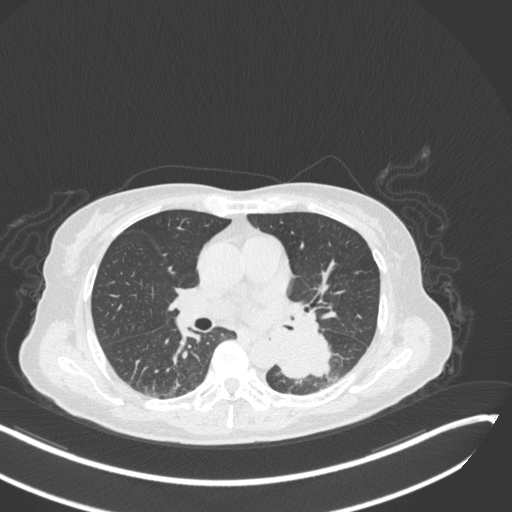
Chest CT, one axial slice; position 148 of 342 along the scan axis; reconstruction kernel B31f; 120 kVp; lung window (W 1500 / L -600 HU); 1 mm slice thickness; 512 × 512 image matrix. Patient: female, 64 years. From the clinical record (not read from this slice): clinical TNM (as recorded): T3 N1 M1; histopathological grade: G3.
Outlined on this slice (rectangle marked by the reading radiologist):
- lung tumour (recorded histology: small cell carcinoma): bounding box [x1, y1, x2, y2] px = [273, 324, 340, 382]